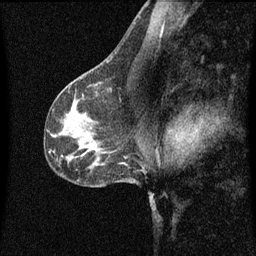
Breast MRI (dynamic contrast-enhanced), one sagittal slice. Position 37 of 60 along the scan axis. Dynamic contrast-enhanced series, image 2 of 3 at this slice position (ordered by acquisition). 1.5 T. TE 4.2 ms, TR 8.4 ms. 2 mm slice thickness. 256 × 256 image matrix, field of view 200 × 200 mm. Female patient, age 41 years.
Annotated regions visible in this slice (semi-automatic segmentation, software-assisted and operator-edited):
- analysis volume of interest (the breast-tissue region the enhancement analysis was run in; not a lesion): bounding box (x1, y1, x2, y2) in pixels: (94, 72, 115, 97)
- tumour enhancement mask (voxels above the 70 % enhancement threshold inside the analysis volume of interest): (96, 88, 111, 97)